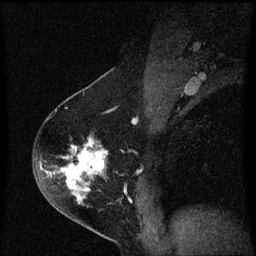
Breast MRI (dynamic contrast-enhanced), one sagittal slice; slice 39 of 60 in the series (ordered by position); dynamic contrast-enhanced series, image 2 of 3 at this slice position (ordered by acquisition); 1.5 T; TE 4.2 ms, TR 8.4 ms; 256 × 256 image matrix, field of view 200 × 200 mm. Female patient, age 54 years. Case-level facts recorded for this patient, not image findings: setting: breast cancer imaged before/during neoadjuvant chemotherapy; receptor status: HER2-positive.
Structures marked on this image (semi-automatic segmentation, software-assisted and operator-edited):
- analysis volume of interest (the breast-tissue region the enhancement analysis was run in; not a lesion): box from (x=34, y=138) to (x=109, y=213) px
- tumour enhancement mask (voxels above the 70 % enhancement threshold inside the analysis volume of interest): (x=50, y=138)–(x=105, y=199)